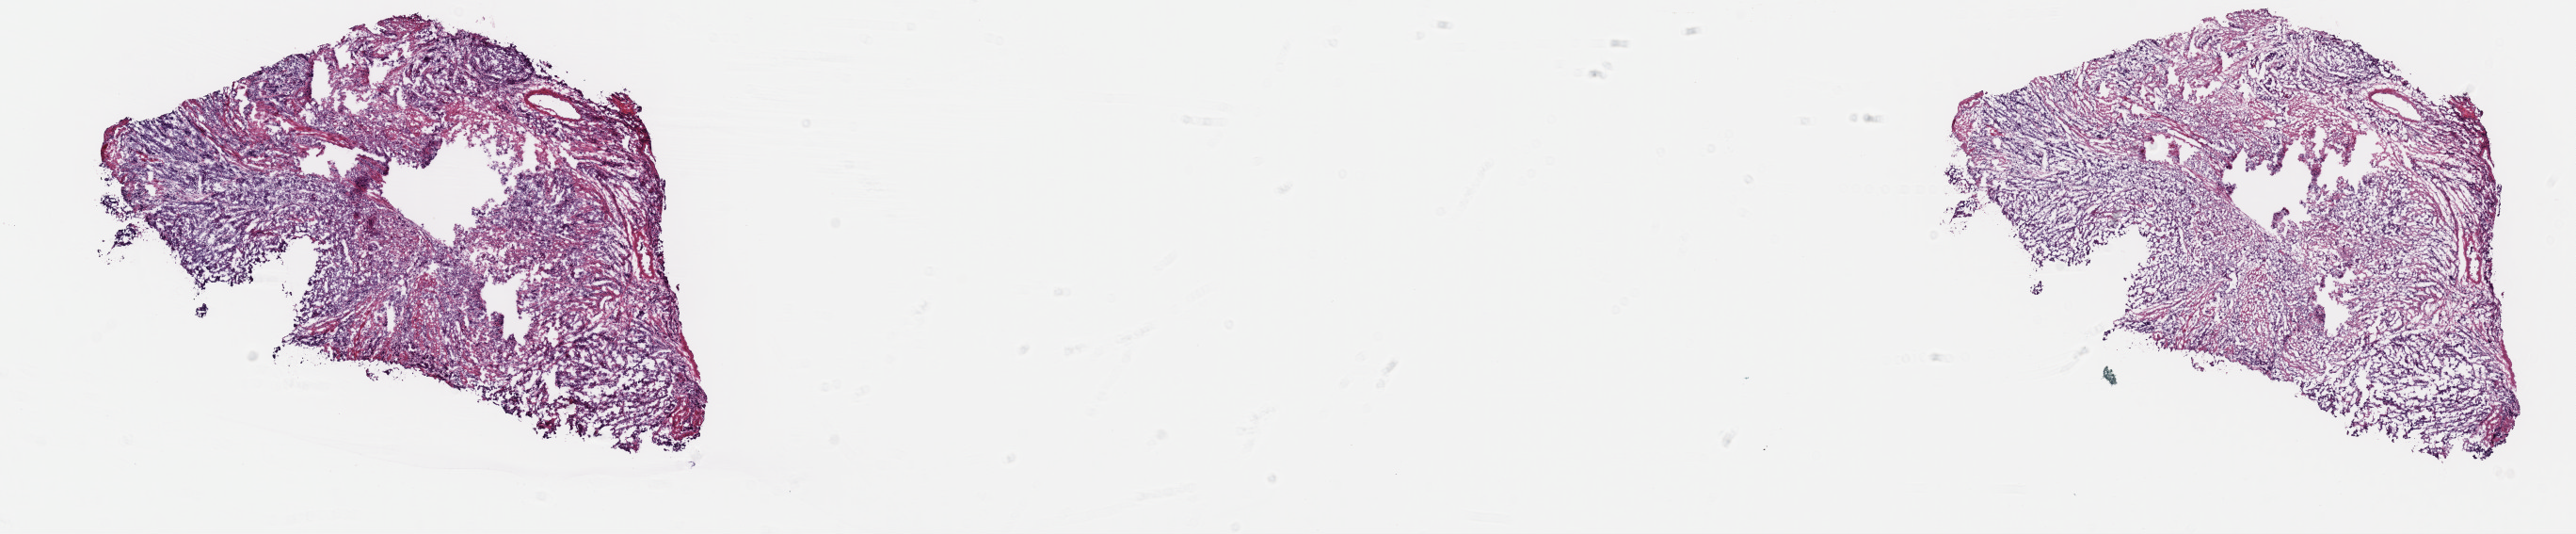
Hematoxylin and eosin (H&E) stained whole-slide image — whole scanned area (about 21.6 x 4.5 mm, from a 40x scan) shown as a low-resolution overview. Frozen section. Uterus, primary tumour sample. Female, age 53 years at initial diagnosis. Histologic grade: G3 (poorly differentiated). Pathologist review of this section (percent, as recorded): tumour cells 90%, tumour nuclei 85%, normal cells 0%, stromal cells 10%, necrosis 0%. Infiltration values recorded for this section: lymphocyte infiltration 1%, monocyte infiltration 0%, neutrophil infiltration 0%.
Diagnosis: Serous cystadenocarcinoma, NOS (endometrium). Lymph nodes positive (case pathology): 1 of 1 examined. FIGO stage: IV.